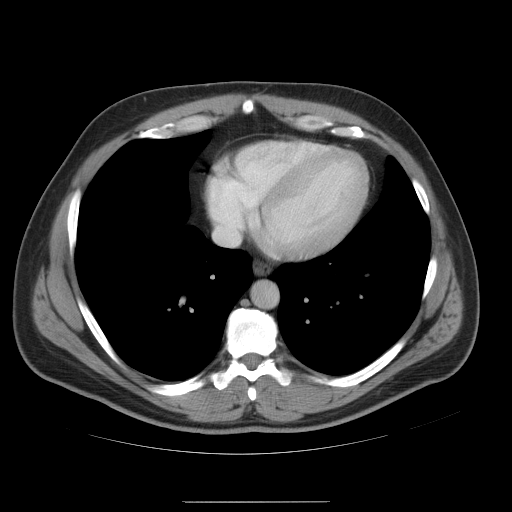
Contrast-enhanced abdominal CT, one axial slice. Position 51 of 54 along the scan axis. Intravenous contrast given. Soft-tissue window (W 400 / L 40 HU). 5 mm slice thickness. 512 × 512 image matrix, field of view 436 × 436 mm. Male patient, age 40 years. Case-level facts recorded for this patient, not image findings: diagnosis: colorectal cancer liver metastases, imaged before liver resection; multiple liver metastases: no; largest metastasis: 15 cm; chemotherapy before resection: no.
Structures marked on this image (outlined manually by an expert reader):
- hepatic veins: bounding box (x1, y1, x2, y2) in pixels: (211, 201, 259, 246)